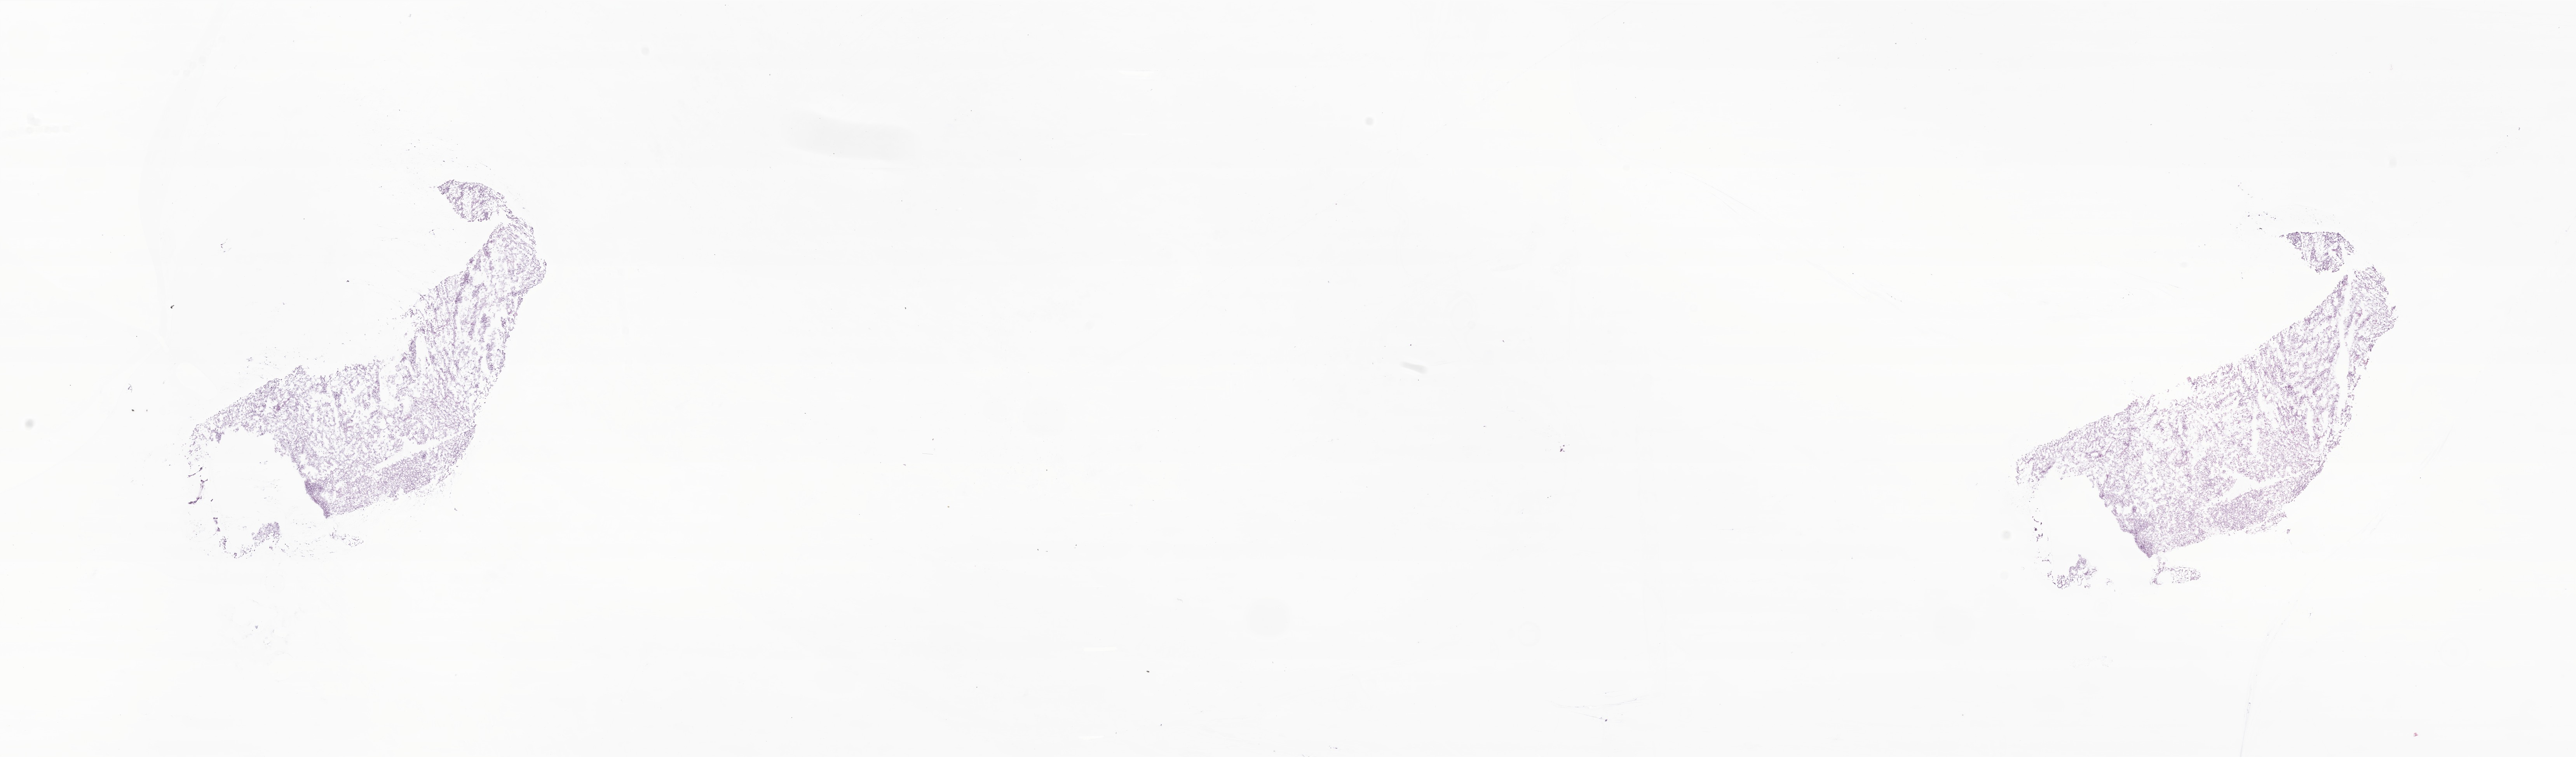
Digitized haematoxylin and eosin-stained section of tumor tissue from the brain — low-resolution overview of the scanned area, about 28.0 x 8.2 mm; cryosection (OCT / tissue freezing medium). Patient female; age 105 months (8 years 9 months).
* diagnosis (ICD-O-3 morphology term): Subependymal giant cell astrocytoma